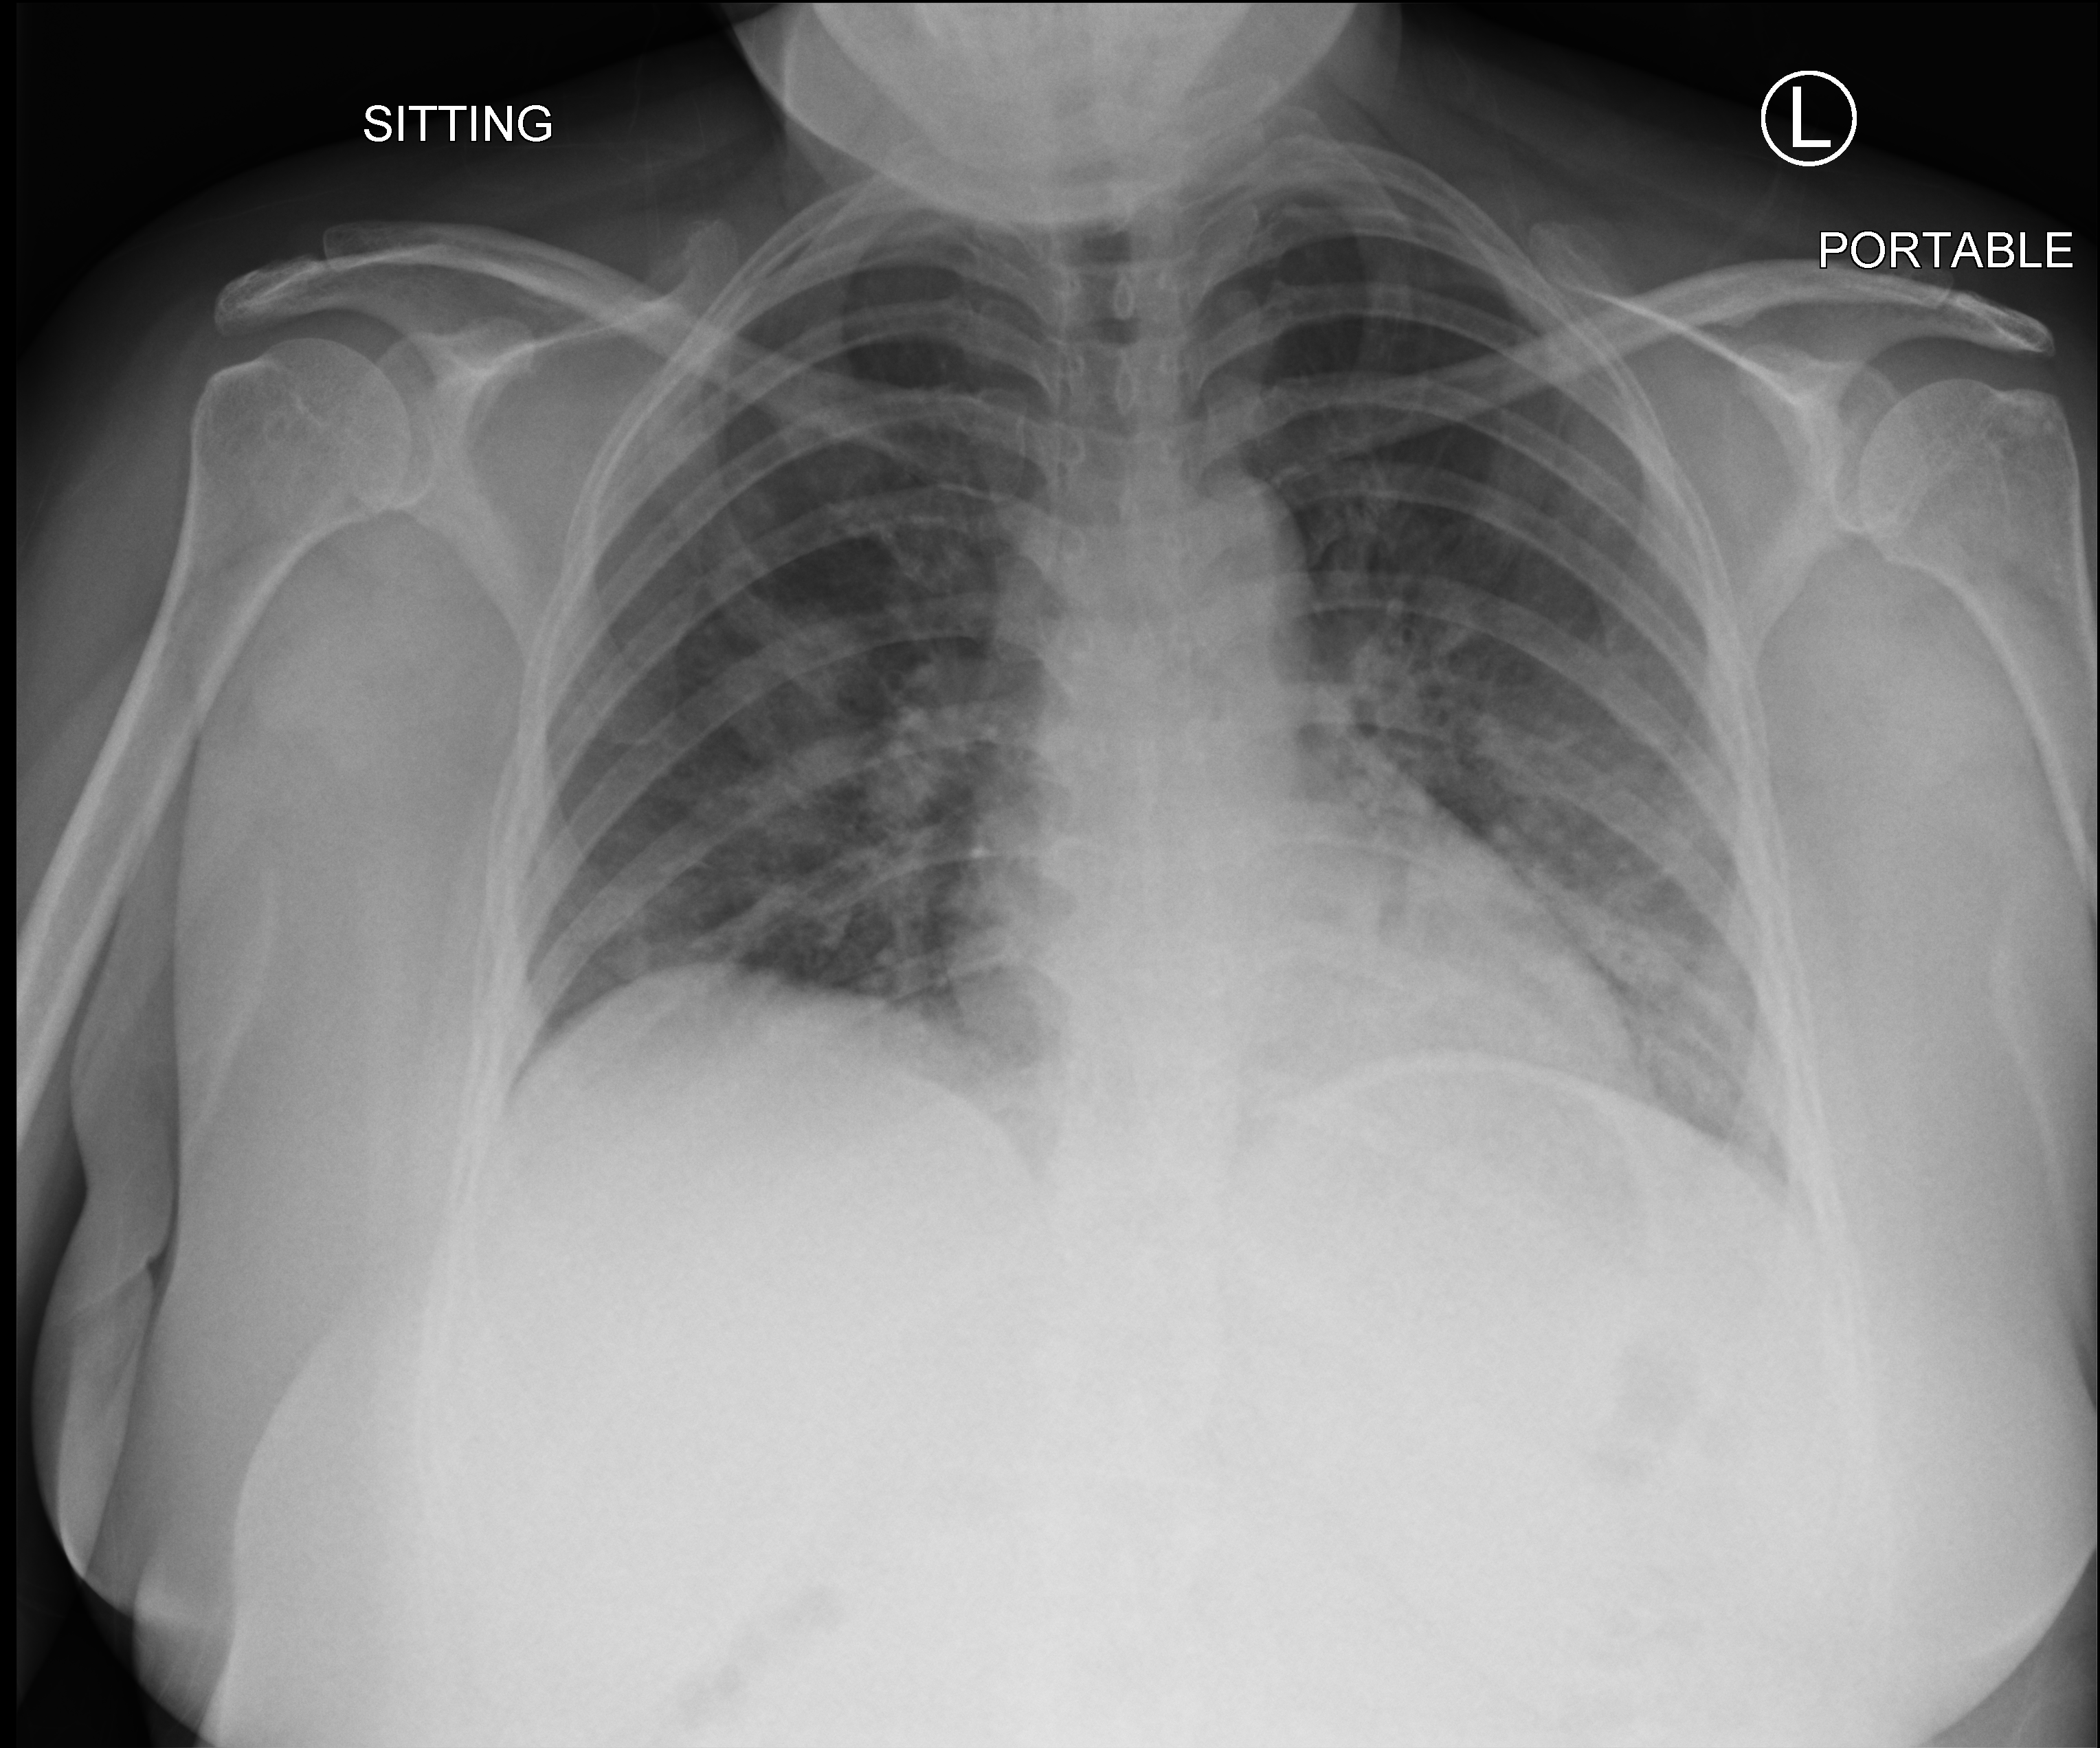
Chest X-ray (portable), anteroposterior (AP) projection. Patient hospitalised with COVID-19; female, aged 18–59 years.
From the hospital-stay record, not from the radiograph (when in the stay this image was taken is not recorded):
- mechanically ventilated during this hospital stay: no